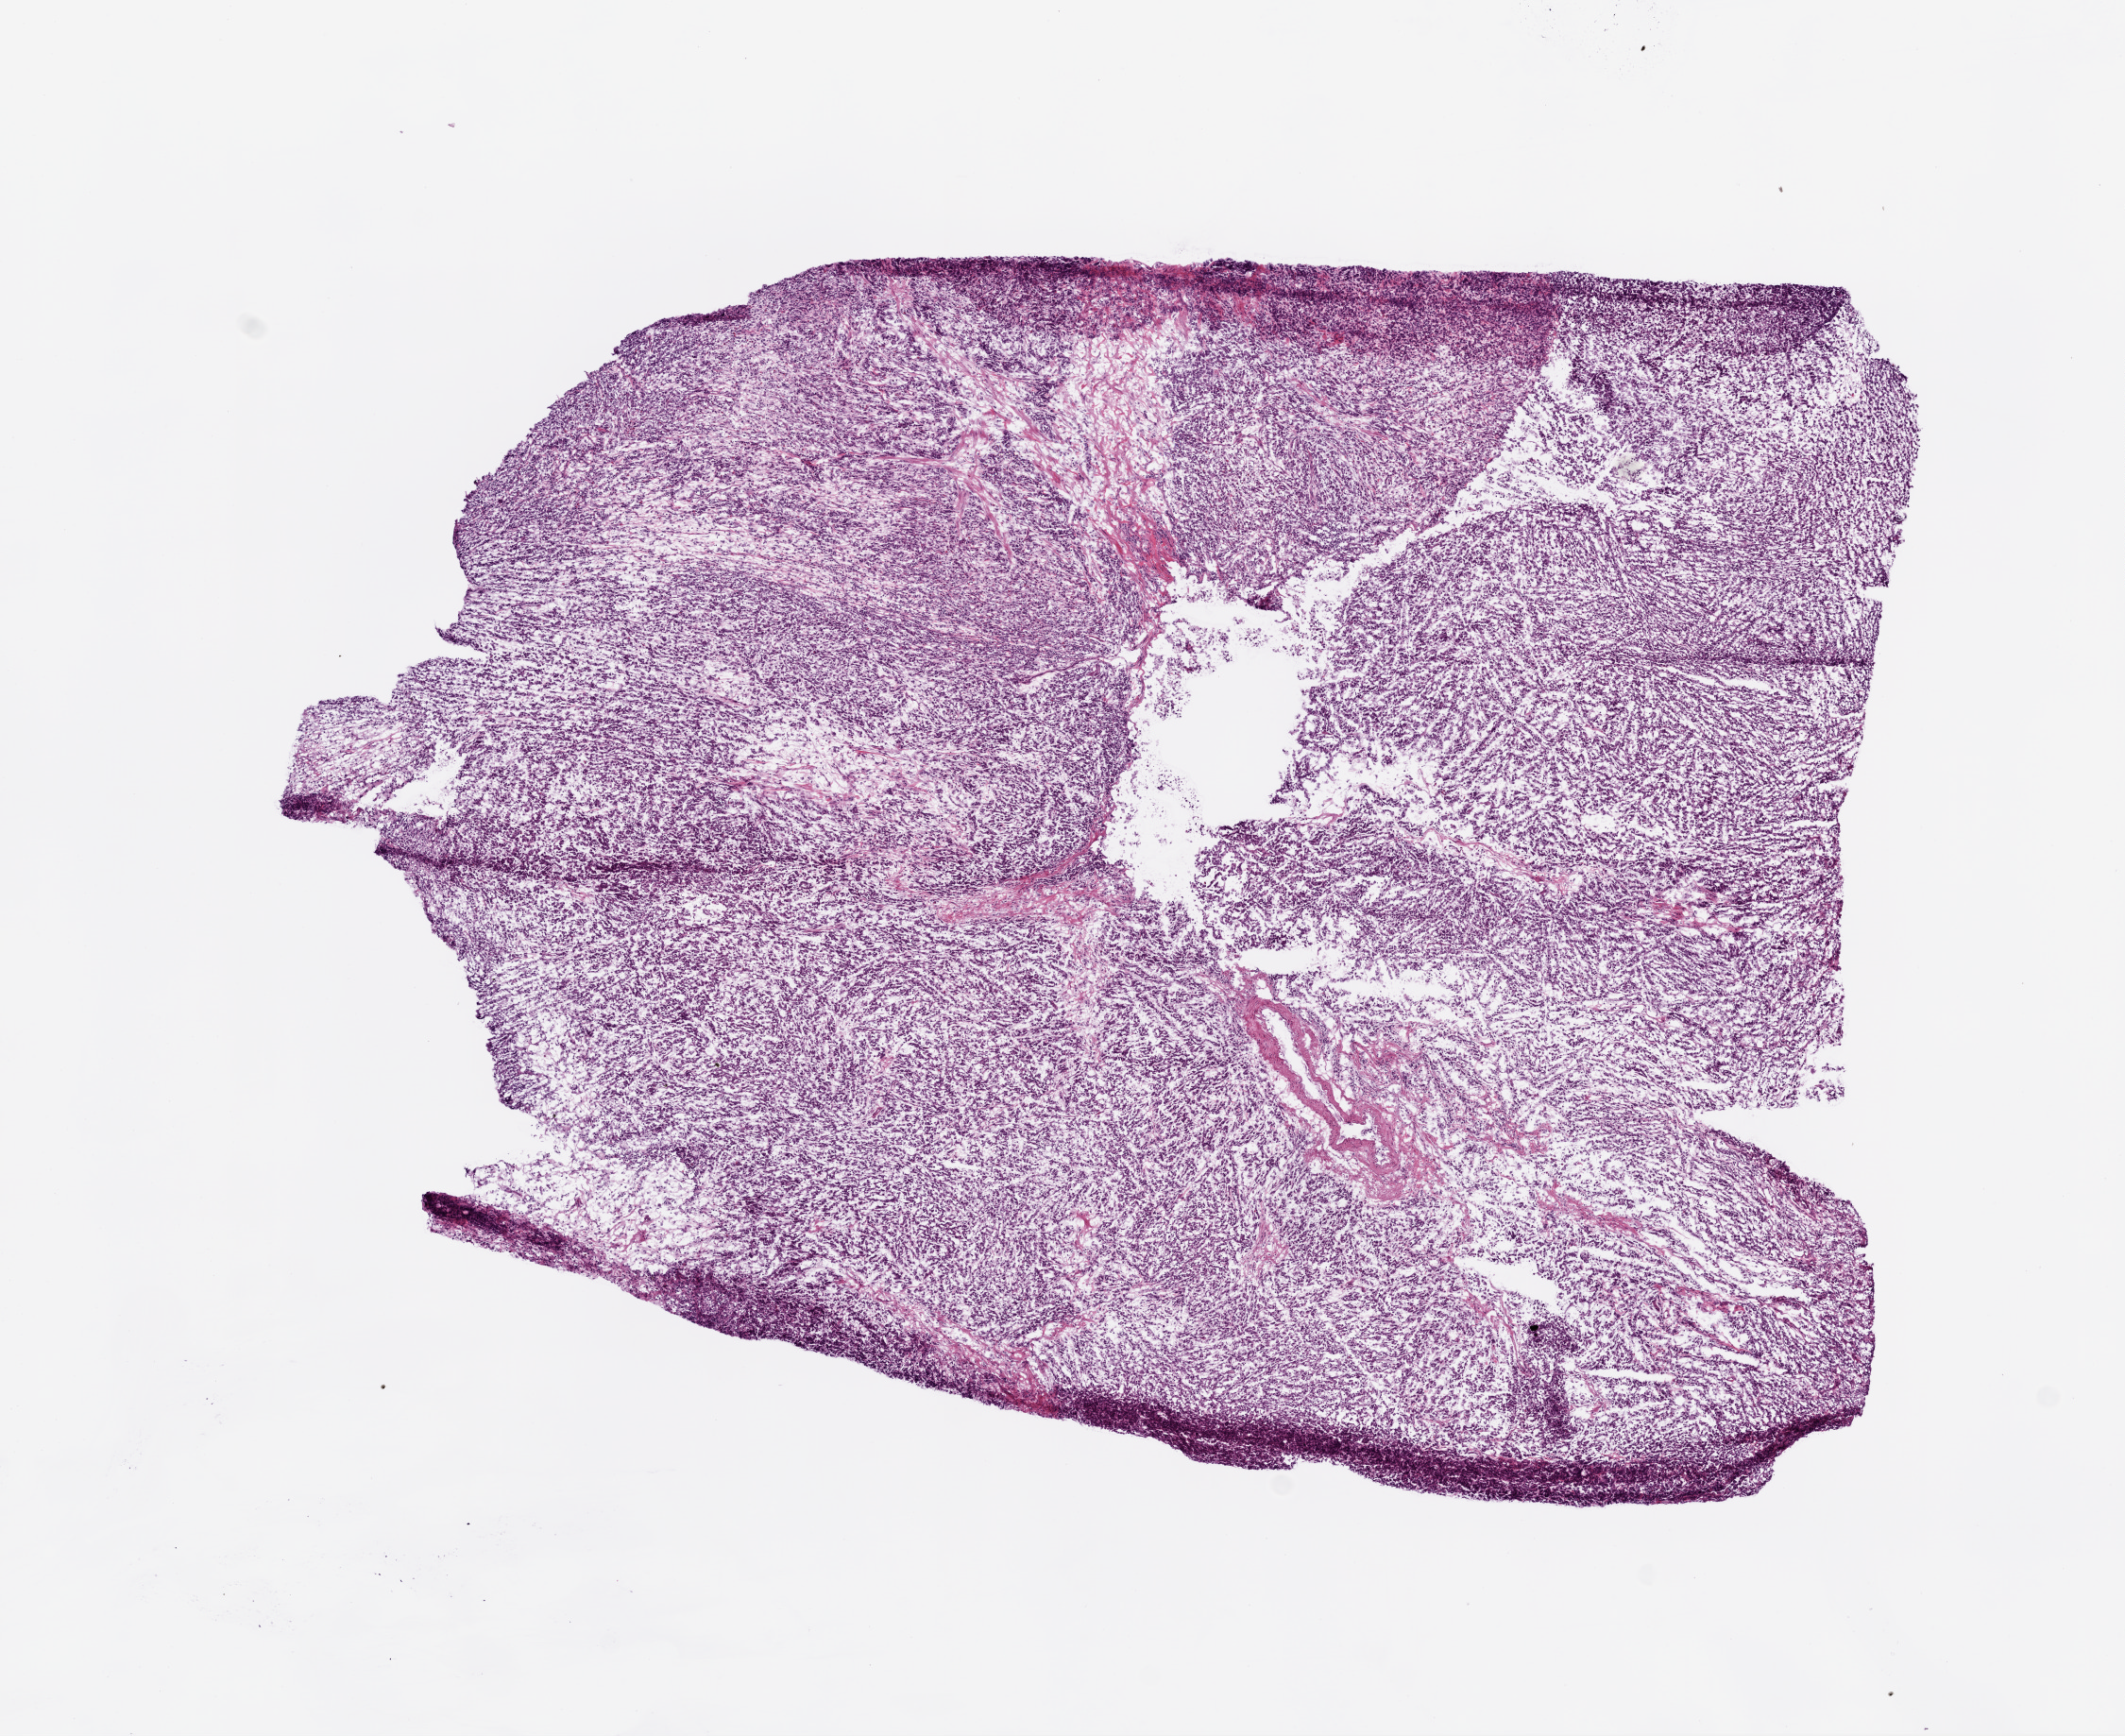
H&E-stained whole-slide image, a low-resolution overview of the entire scanned area, about 9.0 x 7.4 mm (acquisition: 20x scan), frozen section, stomach, primary tumour sample. Male, age 71 years at initial diagnosis. Histologic grade: G3 (poorly differentiated). Pathologist review of this section (percent, as recorded): tumour cells 80%, tumour nuclei 75%, normal cells 0%, stromal cells 15%, necrosis 5%.
- TNM: T2 N0 M0
- diagnosis: Adenocarcinoma, NOS (cardia, NOS)
- AJCC pathologic stage: IB